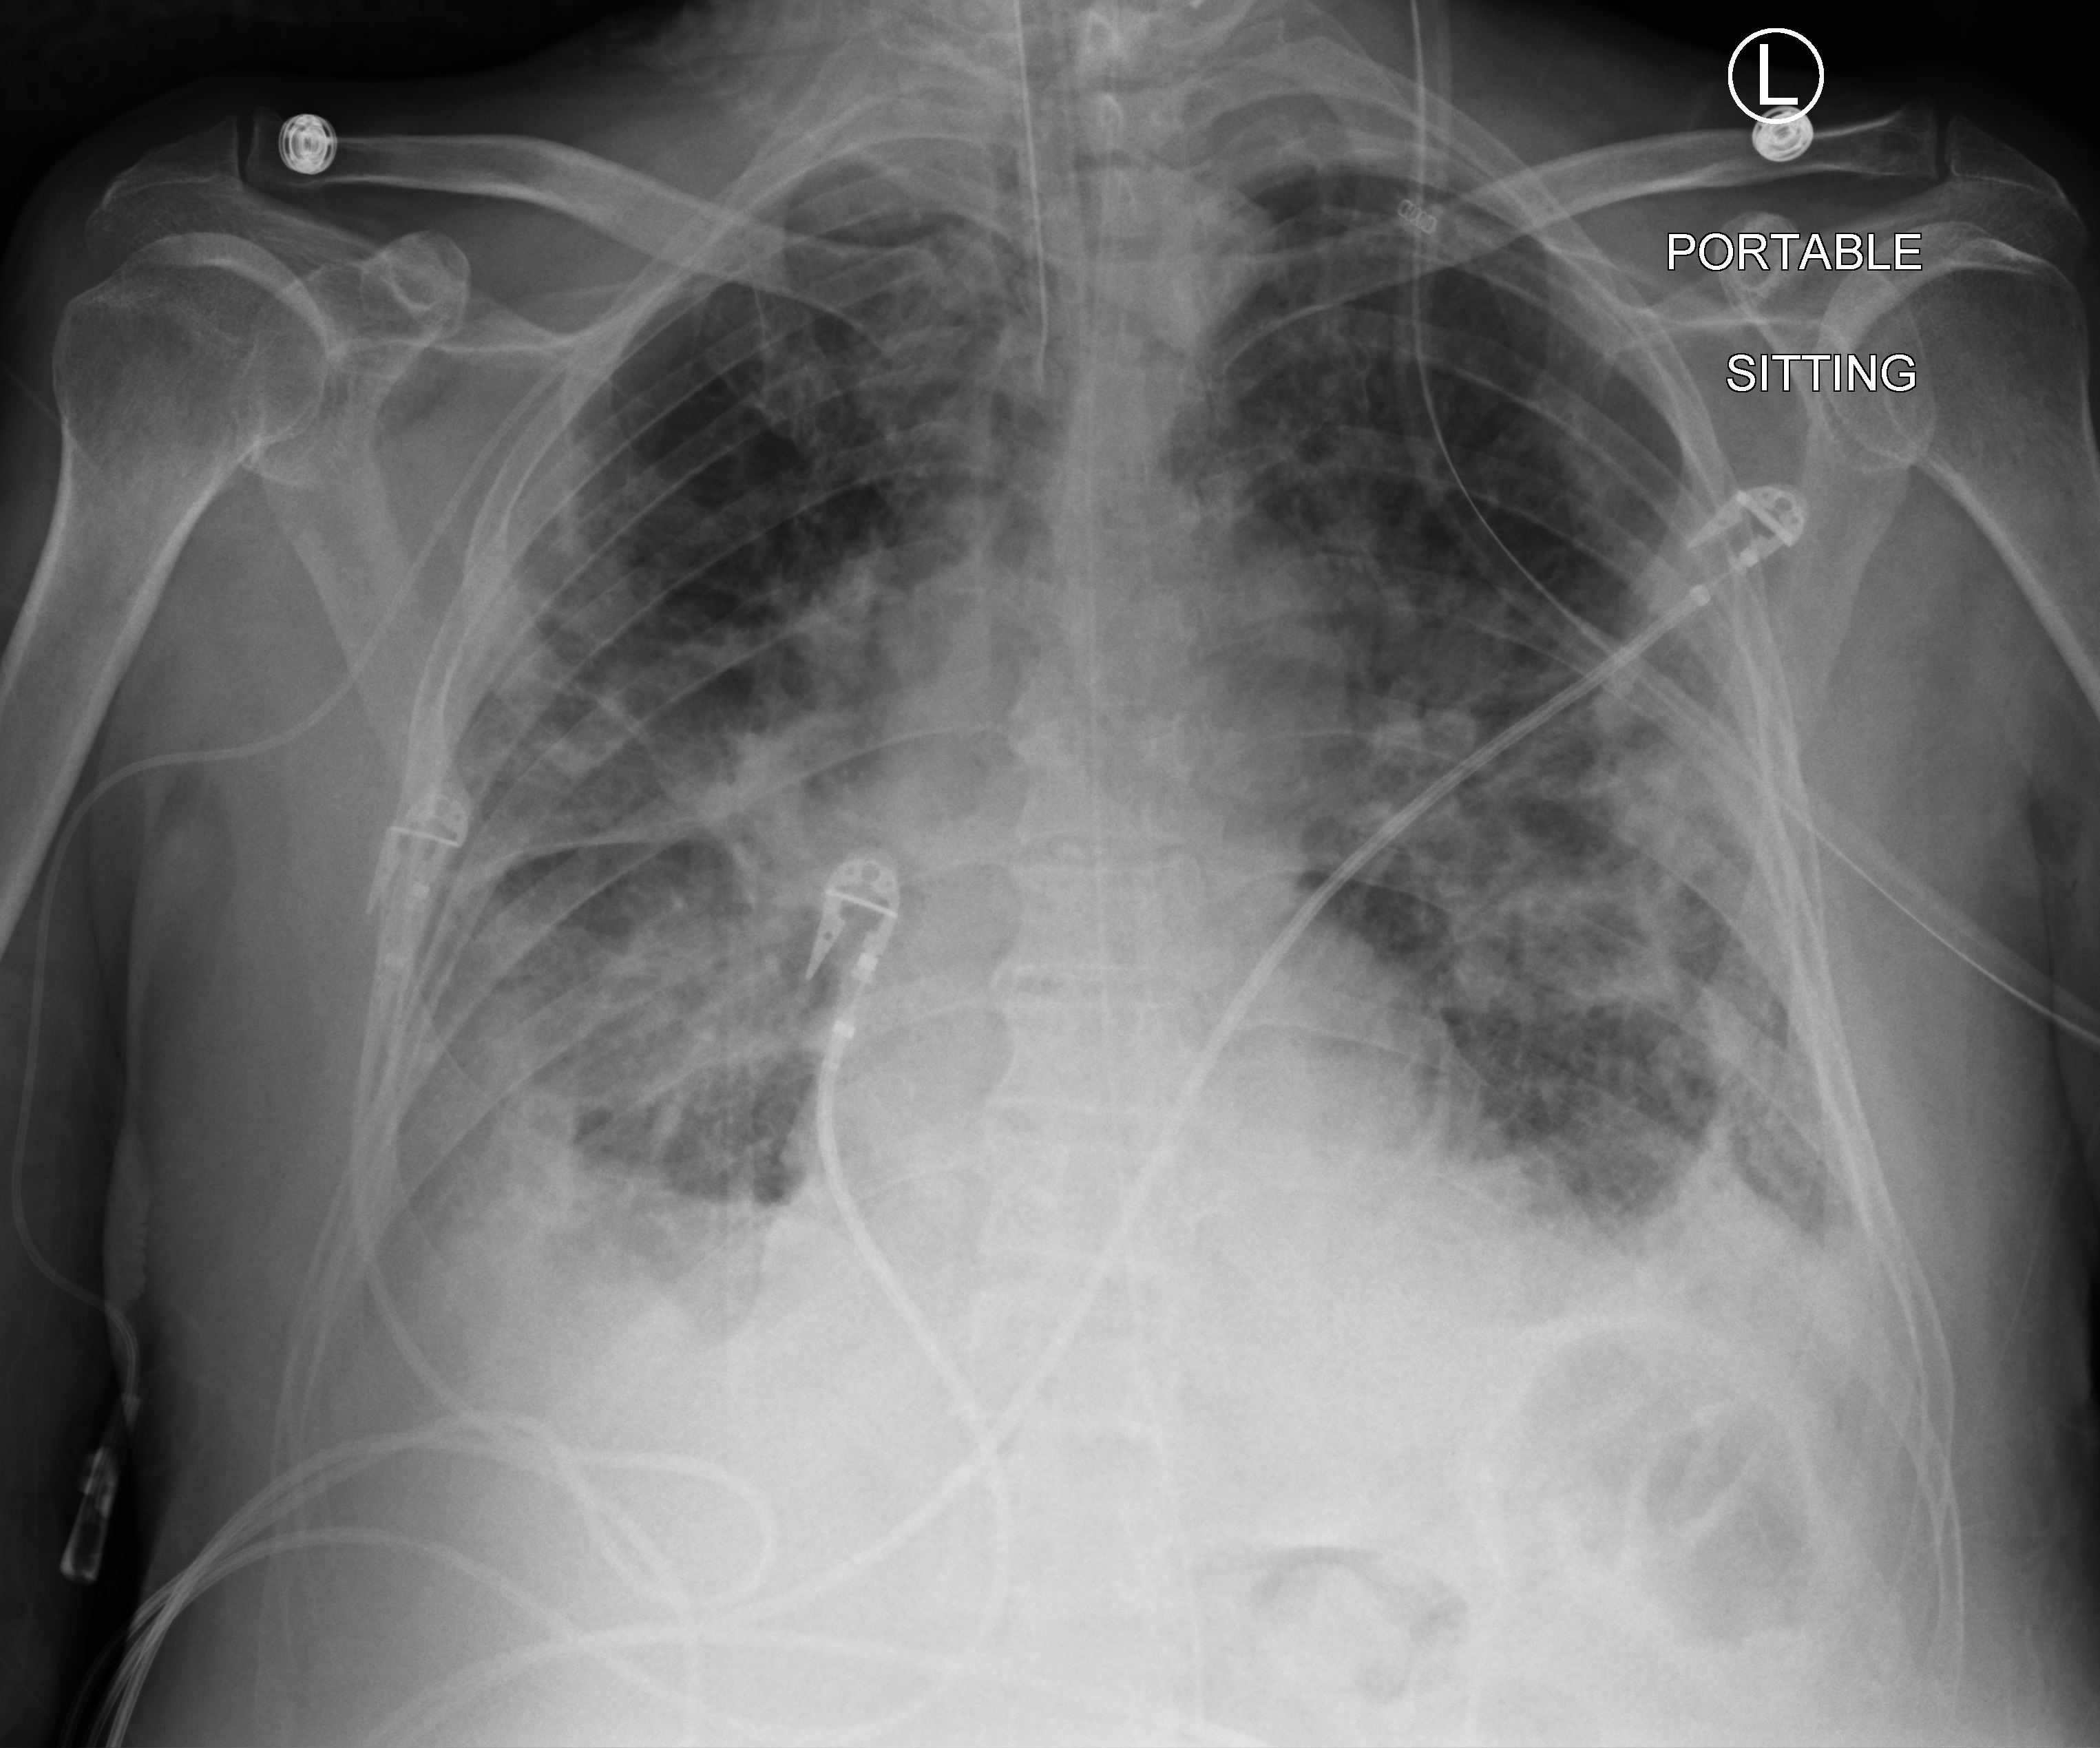
Chest X-ray (portable); anteroposterior (AP) projection. Male patient hospitalised with COVID-19, age 75–90 years.
Admission-level facts for this patient (not findings on this image; timing relative to this image not recorded):
- mechanically ventilated during this hospital stay: yes